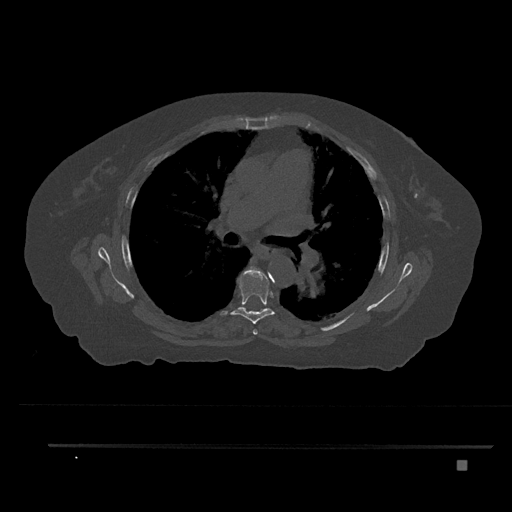
CT including the spine, one axial slice; slice 531 of 797 in the series (ordered by position); 120 kVp; bone window (W 1800 / L 400 HU); 512 × 512 image matrix, field of view 437 × 437 mm. Patient: female, 76 years. Case-level facts recorded for this patient, not image findings: primary cancer: lung; vertebrae with lytic lesions (as recorded): T11, L3.
Structures marked on this image (semi-automatic segmentation, software-assisted and operator-edited):
- T5 vertebra: box from (x=246, y=266) to (x=259, y=335) px
- T6 vertebra: (x=220, y=270)–(x=275, y=324)